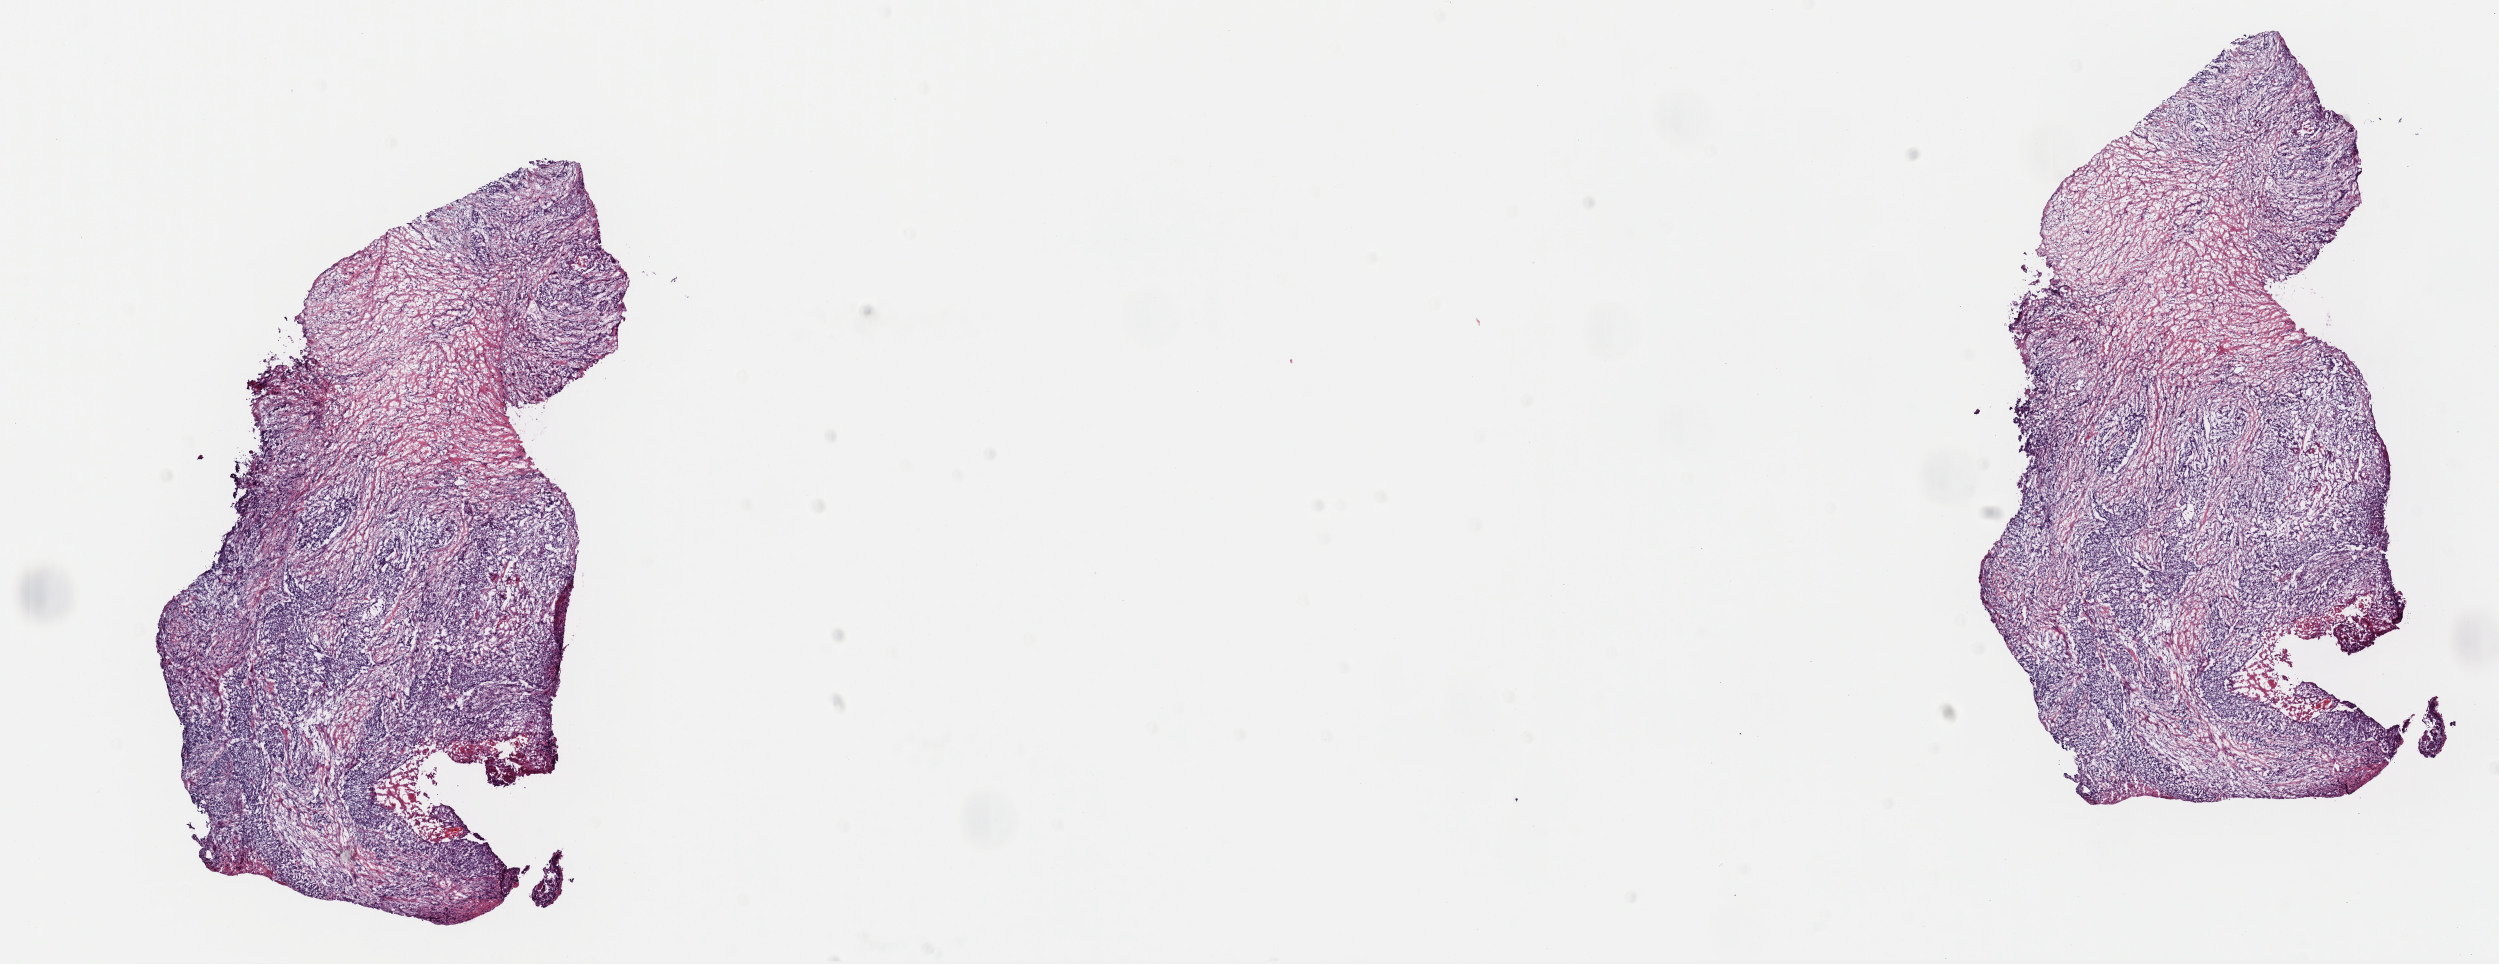
Whole-slide histology image, Hematoxylin and eosin (H&E) stained, whole scanned area (about 19.7 x 7.6 mm) shown as a low-resolution overview; frozen section from the top of the tissue portion; head and neck, primary tumour sample. Patient: male, age at initial diagnosis 60 years. Histologic grade: G2 (moderately differentiated). Composition of this section per pathologist review: tumour cells 80%, tumour nuclei 95%, normal cells 0%, stromal cells 1%, necrosis 19%. Infiltration values recorded for this section: lymphocyte infiltration 2%, monocyte infiltration 0%, neutrophil infiltration 0%.
- AJCC pathologic stage: IVB (7th edition)
- histologic diagnosis: Squamous cell carcinoma, keratinizing, NOS (palate, NOS)